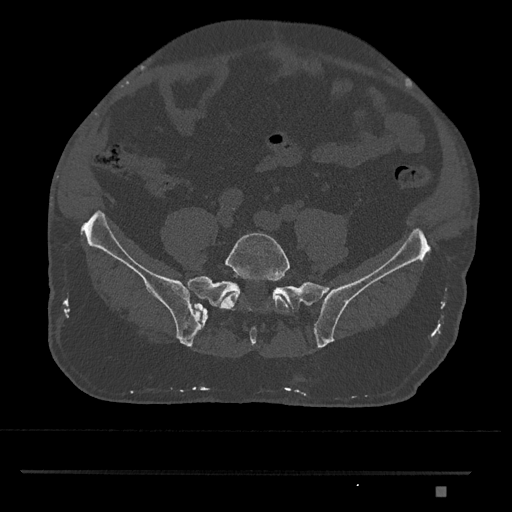
CT including the spine, one axial slice. Slice 534 of 1134 in the series (ordered by position). 120 kVp. Bone window (W 1800 / L 400 HU). 0.5 mm slice thickness. 512 × 512 image matrix, field of view 429 × 429 mm. Patient: male, 65 years. From the clinical record (not read from this slice): primary cancer: prostate.
Outlined on this slice (semi-automatic segmentation, software-assisted and operator-edited):
- L5 vertebra: bounding box [x1, y1, x2, y2] px = [220, 233, 290, 313]